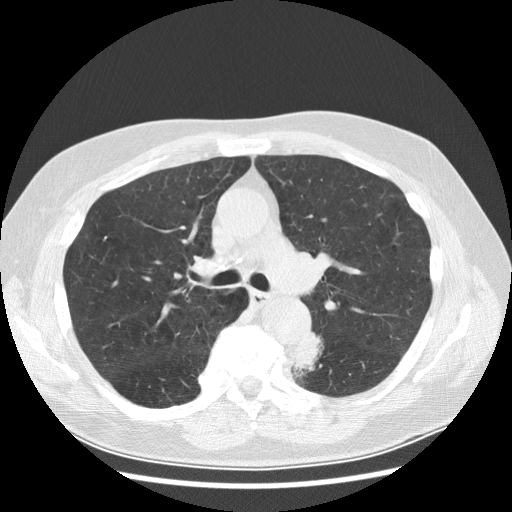
Low-dose screening chest CT, one axial slice. Slice 184 of 282 in the series (ordered by position). 120 kVp. Lung window (W 1500 / L -600 HU). 512 × 512 image matrix.
Annotated regions visible in this slice (manually delineated by an expert):
- lesion 1 (tumor, lower lobe of left lung): box from (x=294, y=332) to (x=324, y=377) px